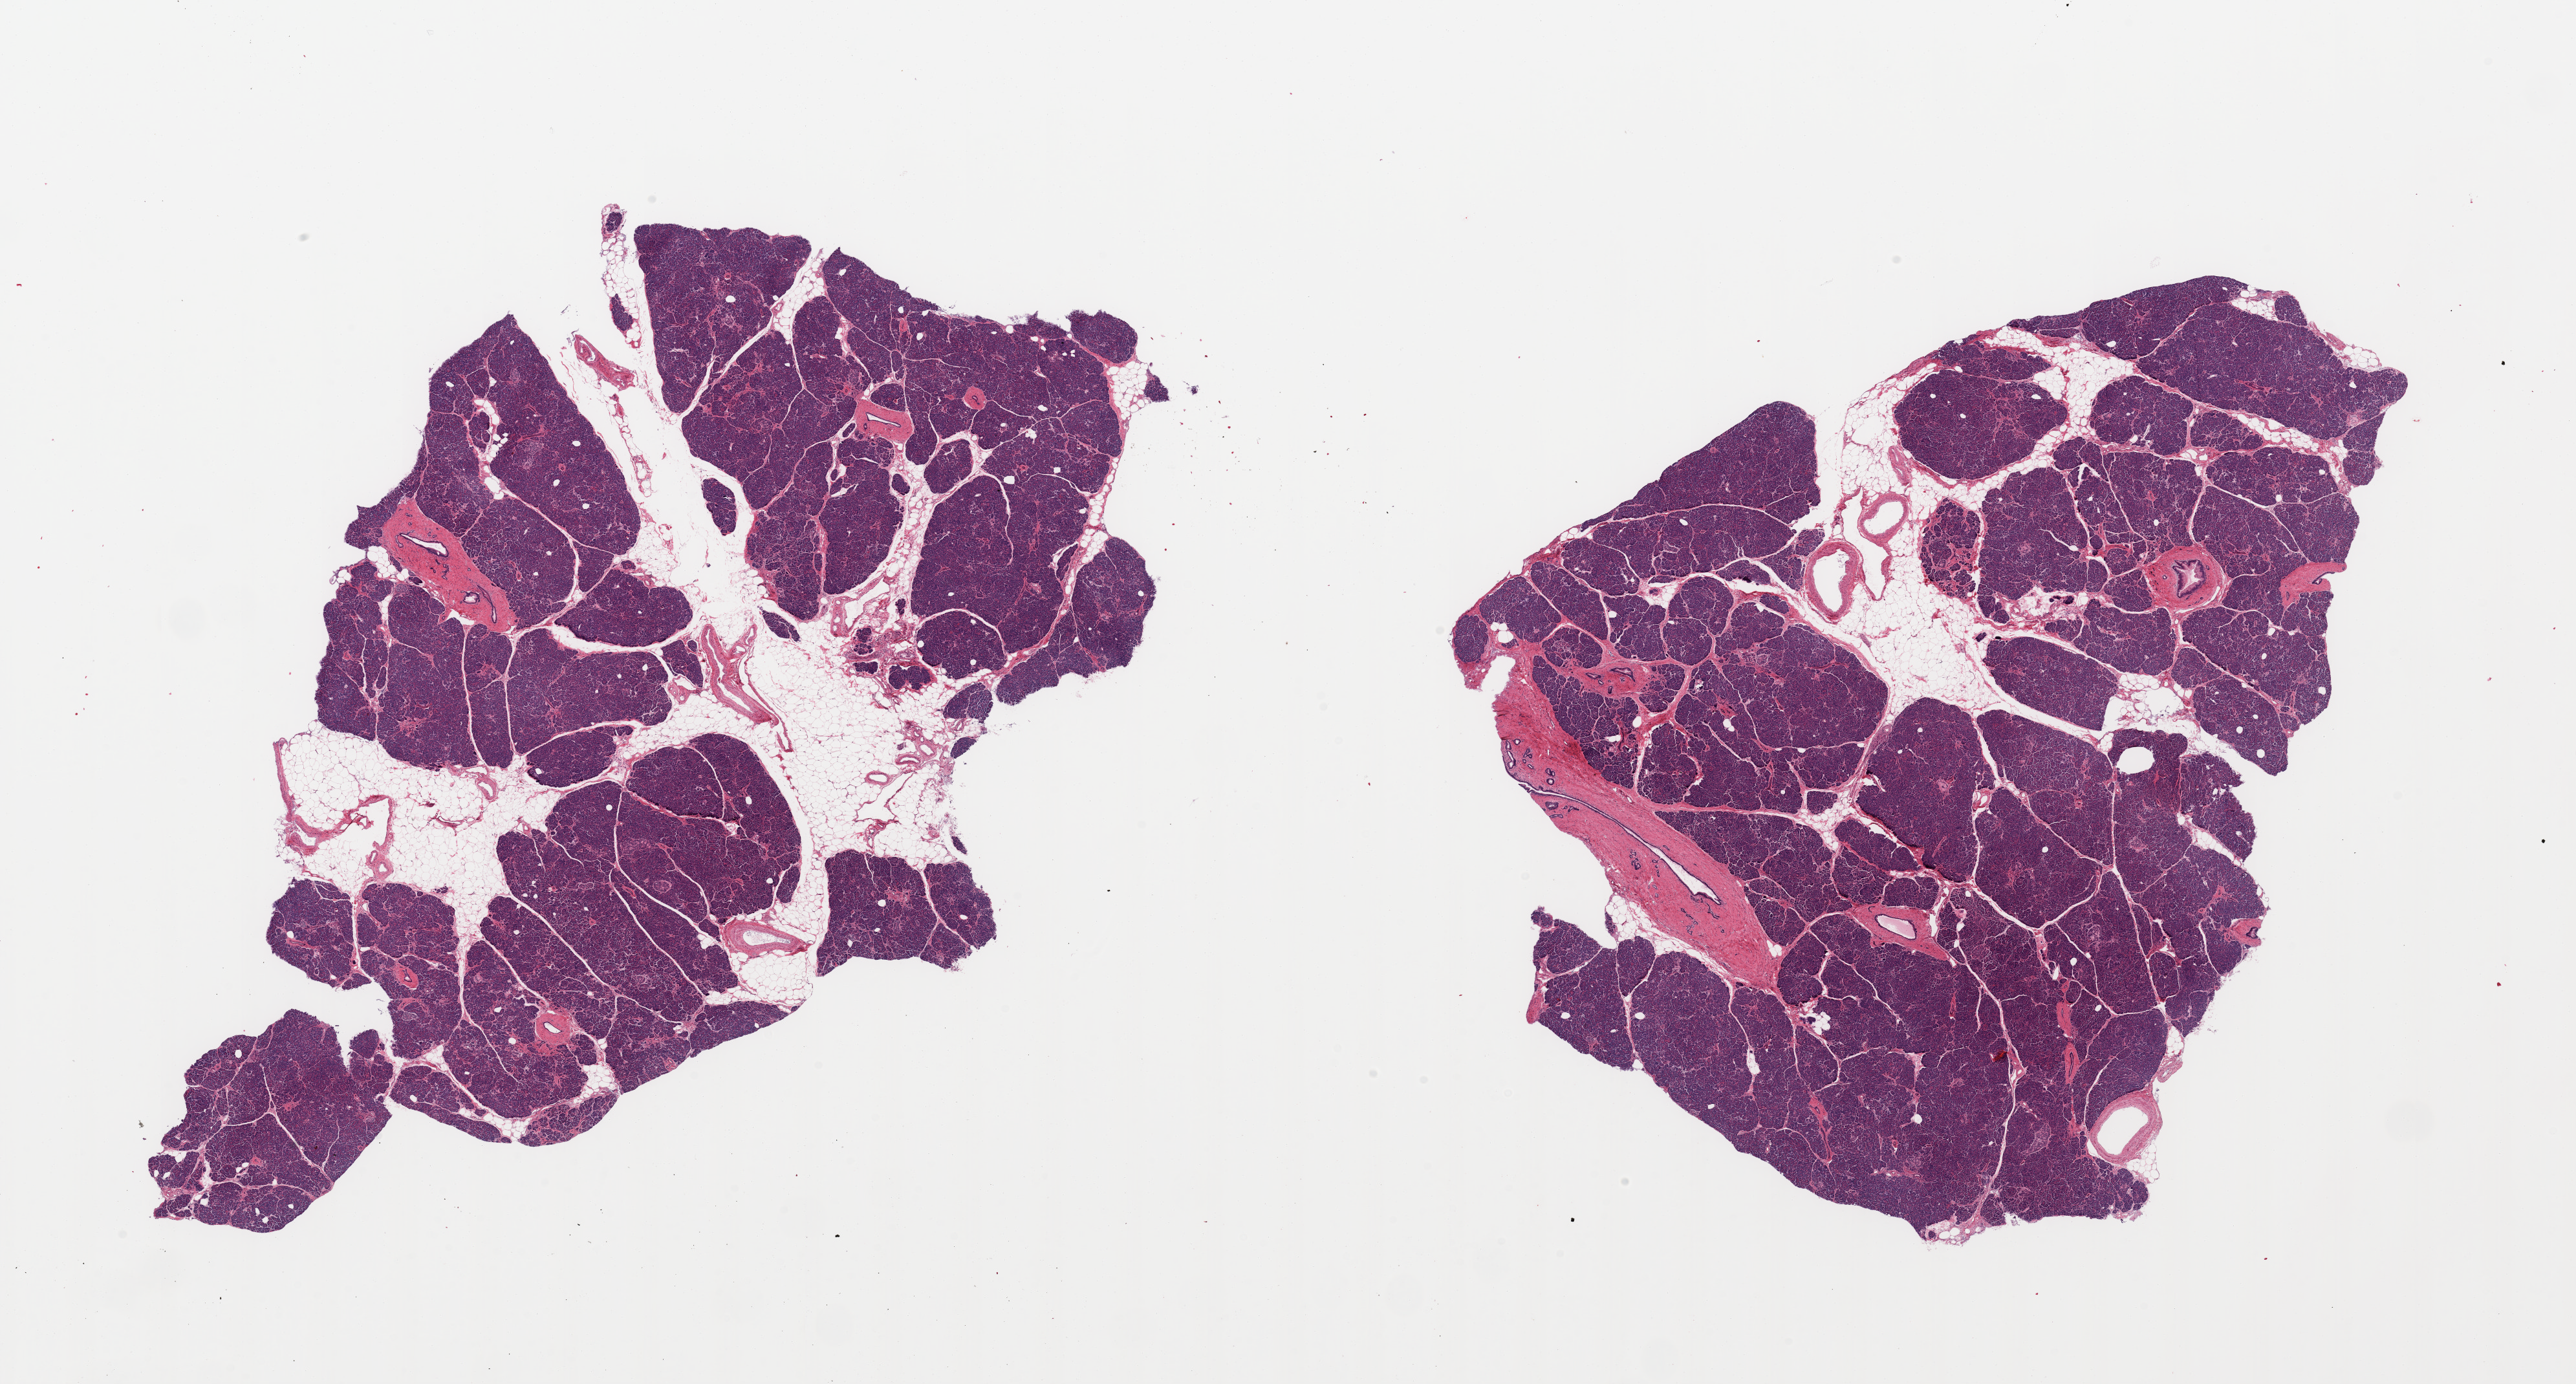
Whole-slide image, H&E stain — shown as a low-resolution overview of the whole scanned area (about 31.5 x 16.9 mm, acquisition: 20x scan), PAXgene-fixed paraffin-embedded (PFPE) section, target tissue: pancreas, tissue donor sample.
* reviewer comment on this tissue sample: 2 pieces; PANin 1A; 10% internal fat